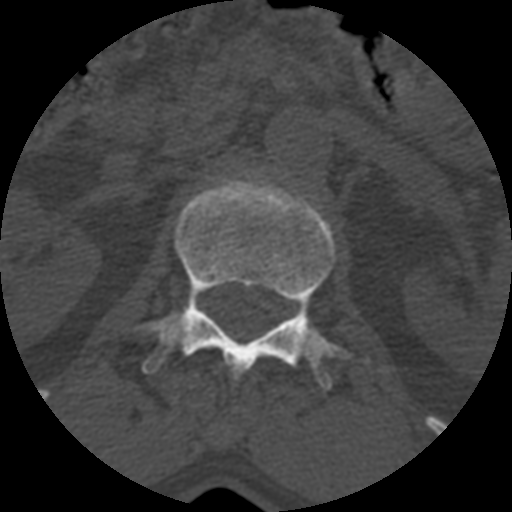
CT including the spine, one axial slice; position 359 of 399 along the scan axis; reconstruction kernel STANDARD; 120 kVp; bone window (W 1800 / L 400 HU); 1.25 mm slice thickness; 512 × 512 image matrix, field of view 160 × 160 mm. Patient age 71 years. From the clinical record (not read from this slice): primary cancer: prostate.
Structures marked on this image (semi-automatically segmented with operator editing):
- L1 vertebra: bounding box <142,180,370,390> (left, top, right, bottom; pixels)